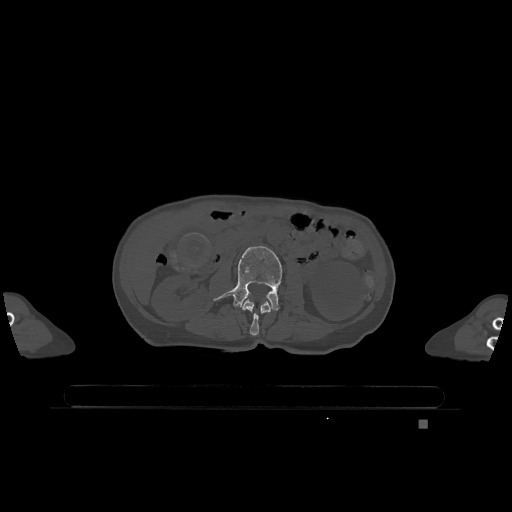
CT including the spine, one axial slice; slice 377 of 1317 in the series (ordered by position); bone window (W 1800 / L 400 HU); 0.5 mm slice thickness; 512 × 512 image matrix, field of view 500 × 500 mm. Patient: female, 74 years. Case-level facts recorded for this patient, not image findings: primary cancer: lung; vertebrae with lytic lesions (as recorded): T1, T4, T5, T6, L4, L5.
Structures marked on this image (semi-automatic segmentation, software-assisted and operator-edited):
- L2 vertebra: bounding box <240,299,273,336> (left, top, right, bottom; pixels)
- L3 vertebra: <213,246,283,310>